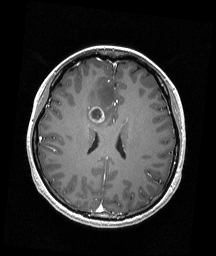
Brain MRI from a brain-tumour surgery series, one axial slice; slice 75 of 192 in the series (ordered by position); T1-weighted post-contrast; 1 mm slice thickness; 216 × 256 image matrix. Case-level facts recorded for this patient, not image findings: histopathology: Astrocytoma; WHO grade: 4; IDH mutation: yes.
Outlined on this slice (outlined manually by an expert reader):
- tumour: bounding box <89,107,104,123> (left, top, right, bottom; pixels)